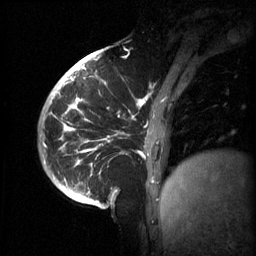
Breast MRI (dynamic contrast-enhanced), one sagittal slice; slice 15 of 60 in the series (ordered by position); 3 images stored at this slice position (order not interpretable as contrast timing); 1.5 T; TE 4.2 ms, TR 11 ms; 2 mm slice thickness; 256 × 256 image matrix. Female patient, age 51 years.
Structures marked on this image (semi-automatically segmented with operator editing):
- analysis volume of interest (the breast-tissue region the enhancement analysis was run in; not a lesion): bounding box <63,80,187,201> (left, top, right, bottom; pixels)
- tumour enhancement mask (voxels above the 70 % enhancement threshold inside the analysis volume of interest): <68,80,154,185>